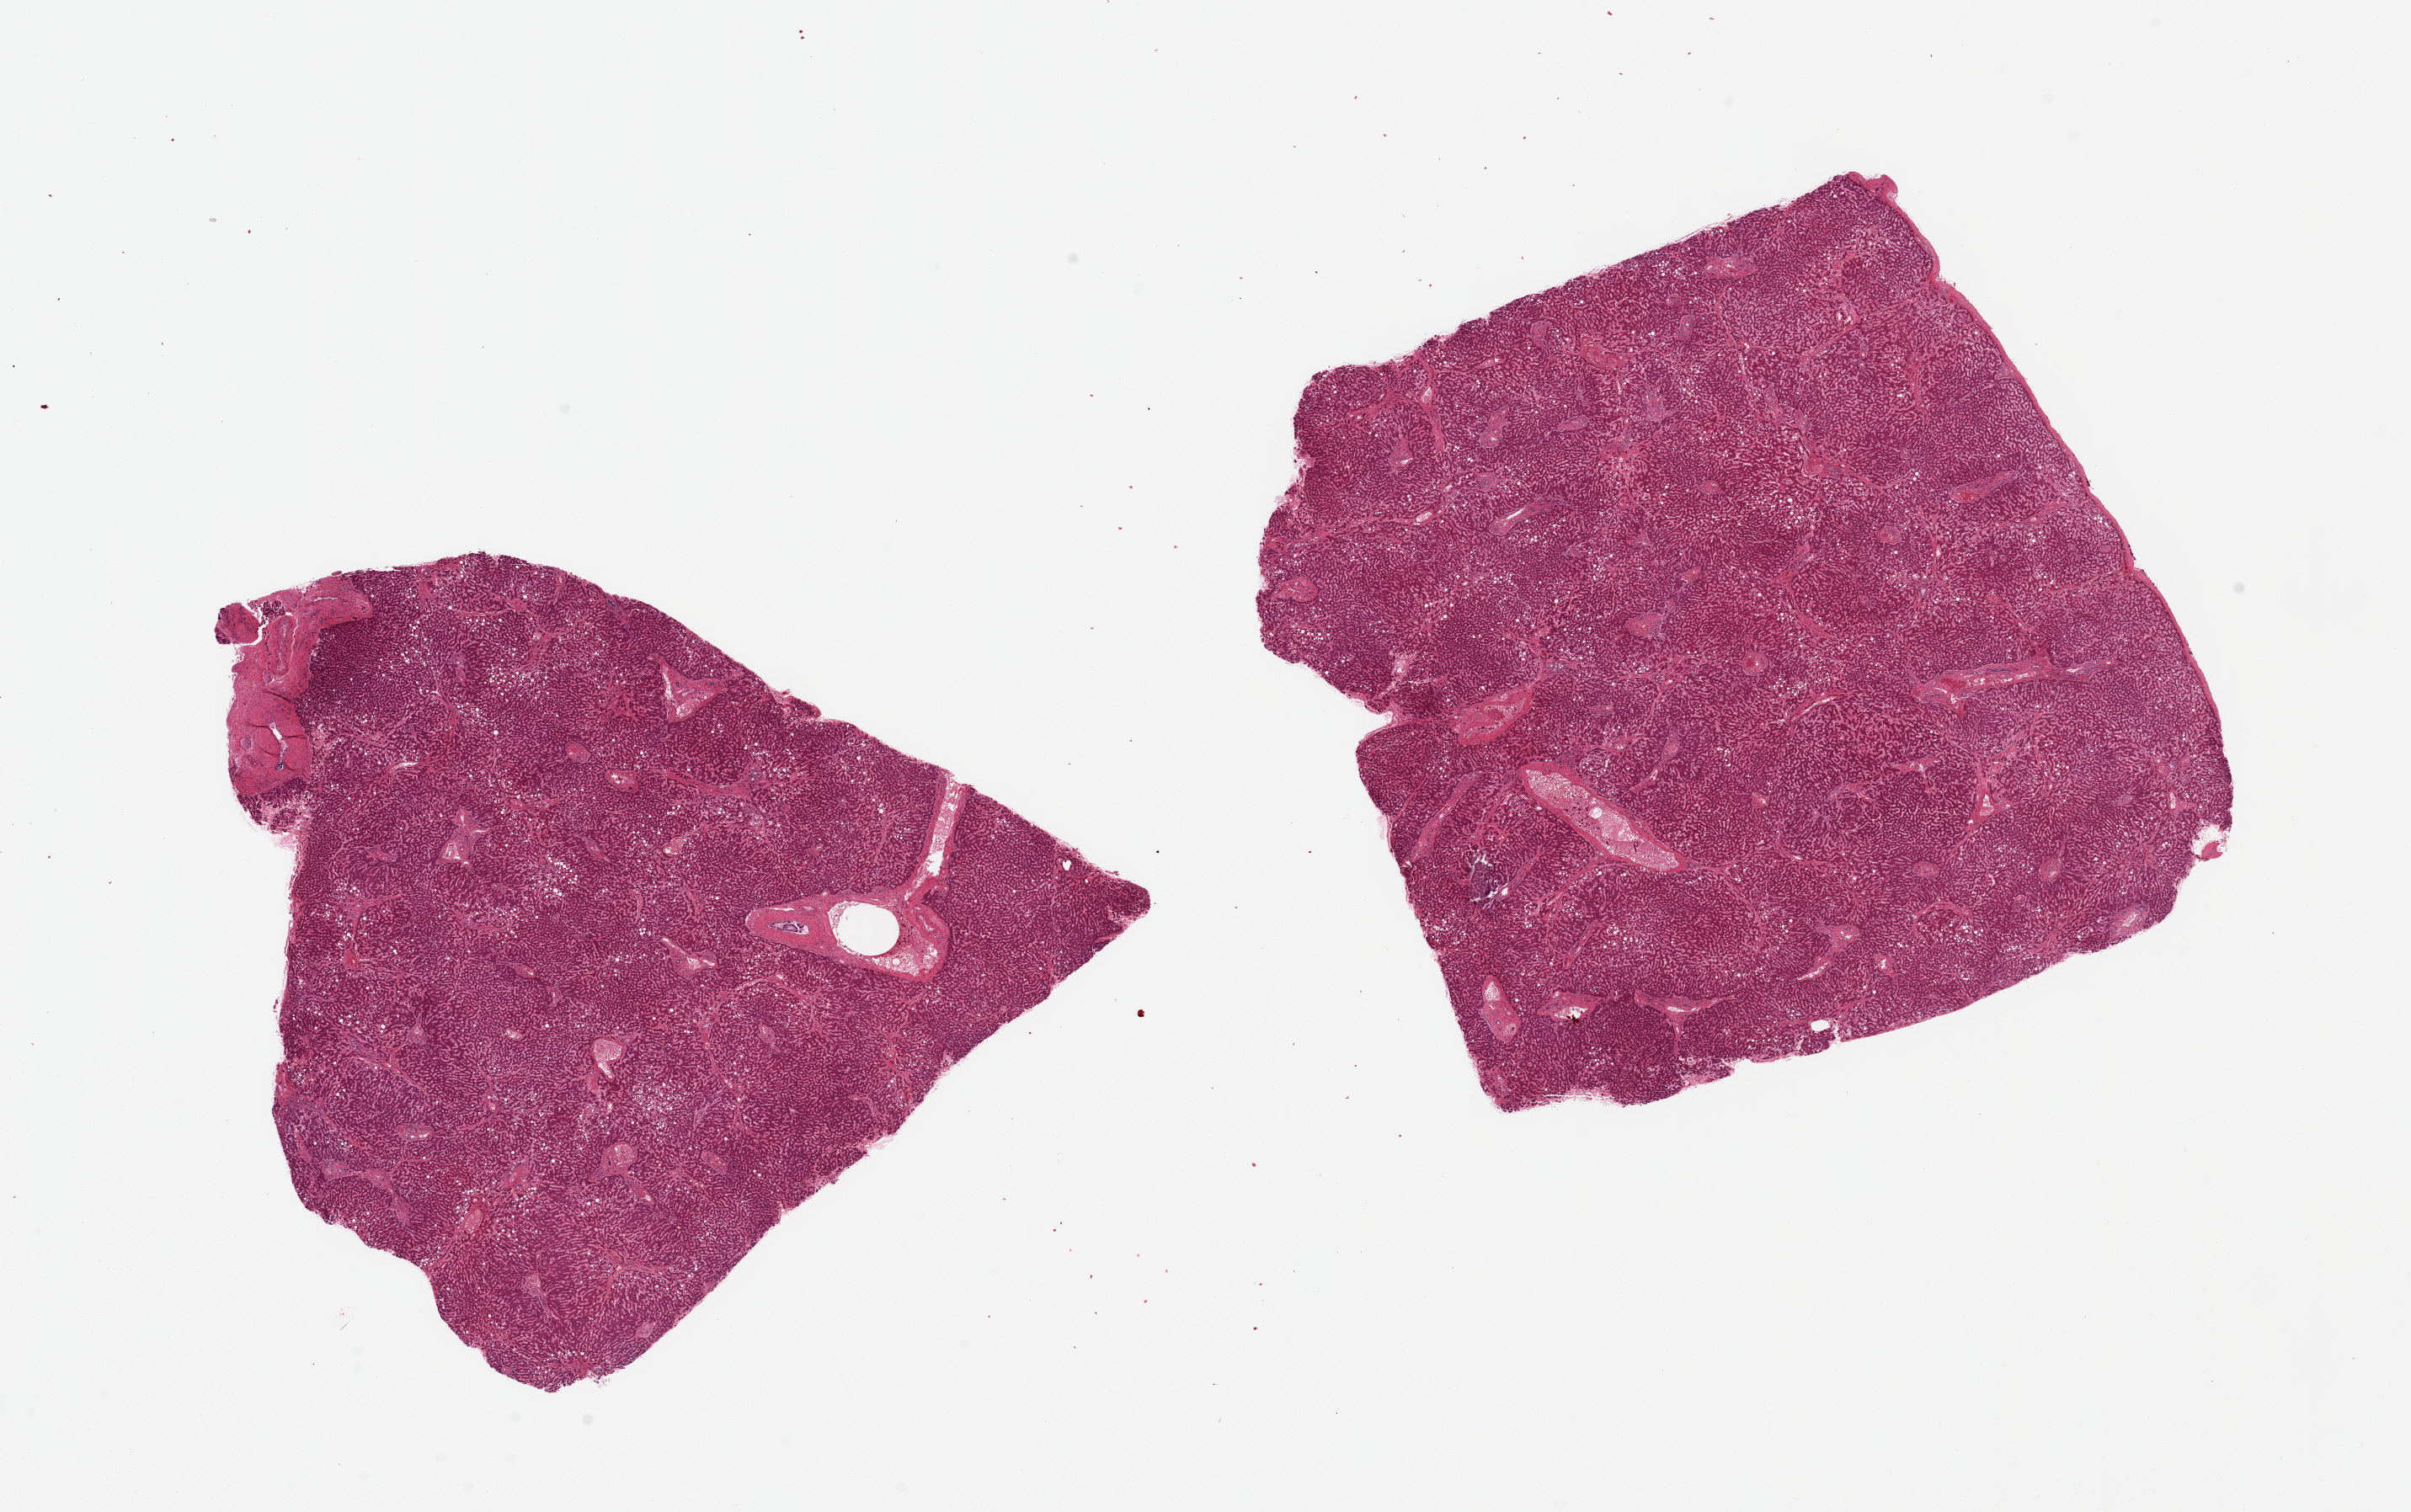
Digitized hematoxylin and eosin (H&E)-stained section, low-resolution overview of the scanned area, about 22.6 x 14.2 mm; PAXgene-fixed, paraffin-embedded tissue; section of liver (target tissue); donor tissue sample.
- pathologist's review note for this sample: 2 pieces, 9x8 & 8x7mm; ~20% macrovesciular steatosis